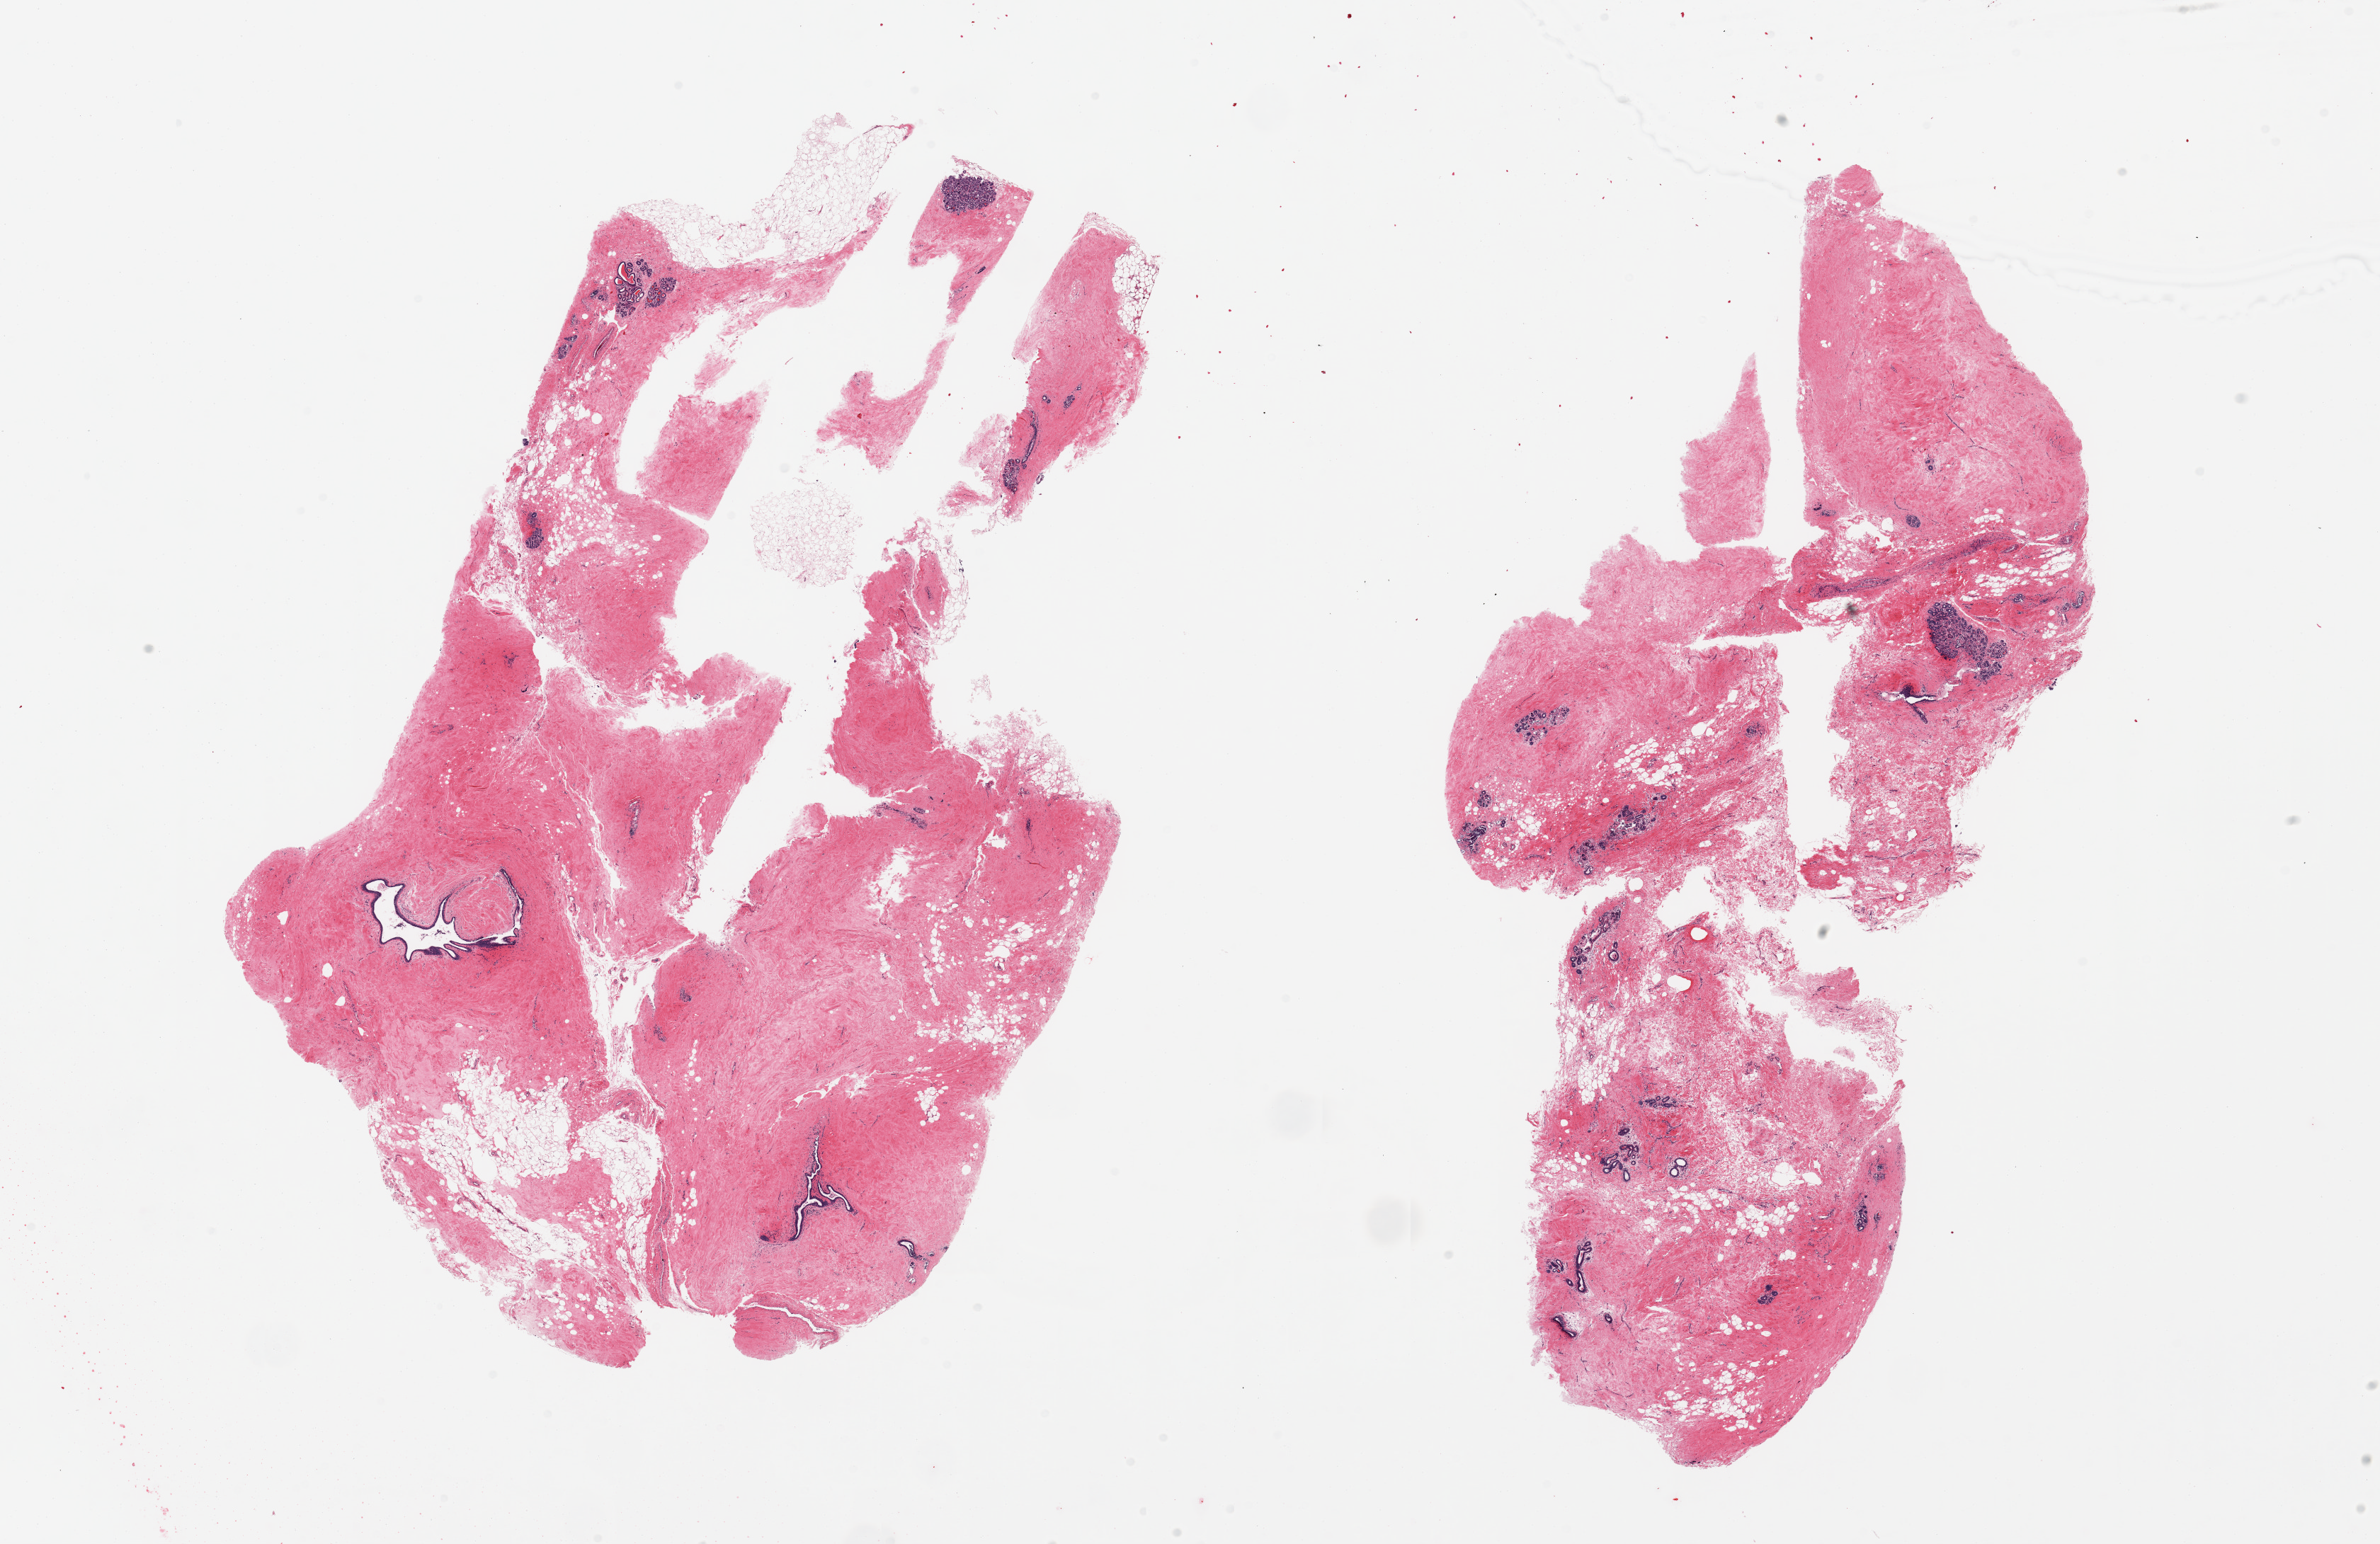
Digitized haematoxylin and eosin-stained section, whole scanned area (about 26.6 x 17.2 mm, slide scanned at 20x) shown as a low-resolution overview; PAXgene-fixed, paraffin-embedded tissue; sampled site (target tissue): breast; donor tissue sample.
Review note (as recorded): 2 pieces; predominantly fibrocollagenous stroma with benign ductal/lobular elements, some fat.